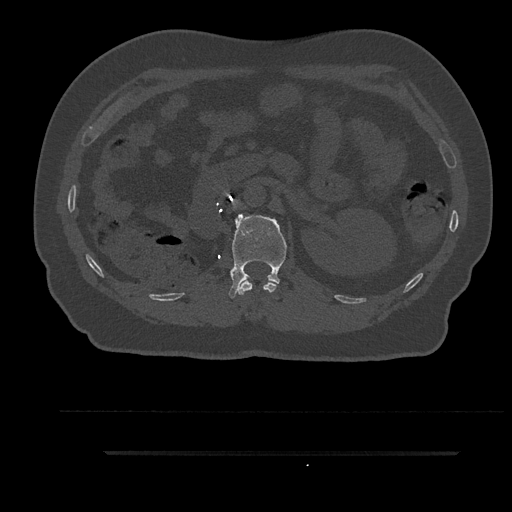
CT including the spine, one axial slice; position 192 of 797 along the scan axis; 120 kVp; bone window (W 1800 / L 400 HU); 512 × 512 image matrix. Patient: male, 63 years. Case-level facts recorded for this patient, not image findings: primary cancer: renal.
Structures marked on this image (semi-automatically segmented with operator editing):
- L1 vertebra: box from (x=228, y=214) to (x=287, y=298) px
- T12 vertebra: (x=239, y=280)–(x=277, y=295)